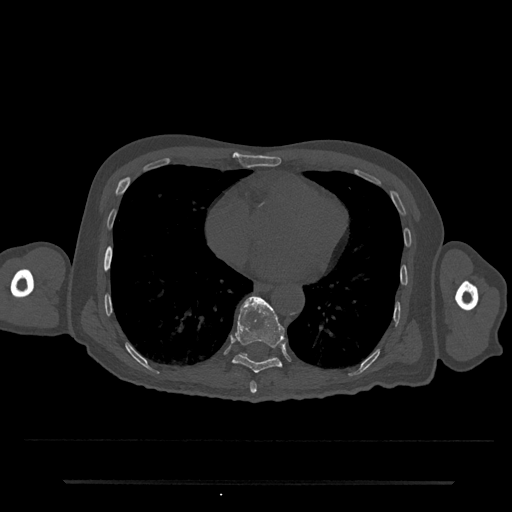
CT including the spine, one axial slice. Slice 360 of 797 in the series (ordered by position). Reconstruction kernel Br40s/3. Bone window (W 1800 / L 400 HU). 0.5 mm slice thickness. 512 × 512 image matrix, field of view 427 × 427 mm. Patient: male, 74 years. Case-level facts recorded for this patient, not image findings: primary cancer: prostate.
Outlined on this slice (semi-automatic segmentation, software-assisted and operator-edited):
- T10 vertebra: bounding box [x1, y1, x2, y2] px = [241, 353, 247, 356]
- T8 vertebra: [250, 381, 257, 394]
- T9 vertebra: [233, 295, 285, 373]